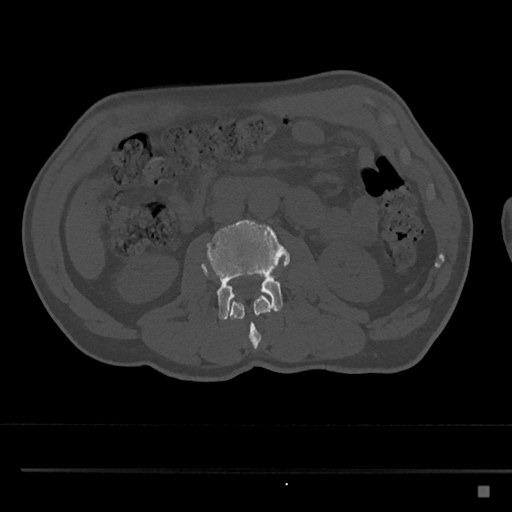
CT including the spine, one axial slice. Position 722 of 797 along the scan axis. Reconstruction kernel Br40s/3. 120 kVp. Bone window (W 1800 / L 400 HU). 0.5 mm slice thickness. 512 × 512 image matrix, field of view 391 × 391 mm. Patient: male, 59 years. Case-level facts recorded for this patient, not image findings: primary cancer: prostate.
Outlined on this slice (semi-automatically segmented with operator editing):
- L2 vertebra: bounding box [x1, y1, x2, y2] px = [202, 265, 272, 350]
- L3 vertebra: [201, 220, 290, 320]